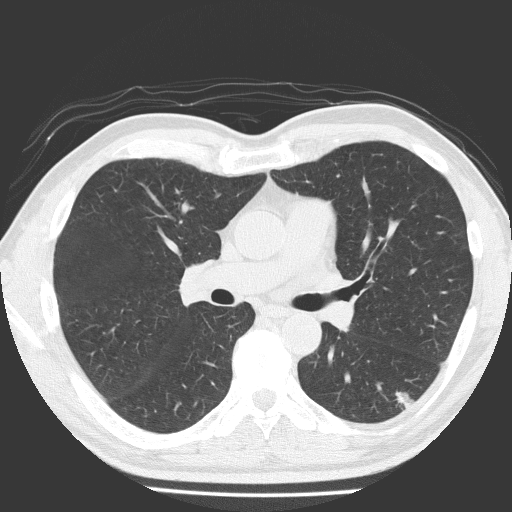
Low-dose screening chest CT, axial slice, baseline annual screen, lung window (W 1500 / L -600 HU), 2 mm slice thickness, lung (sharp) reconstruction kernel (FC51), slice 79 of 184 in the series. Male participant, aged 58 years at enrolment.
- Expert-annotated lung lesion, box from (x=365, y=374) to (x=427, y=423) px.
- The screening reader recorded 4 non-calcified nodules or masses ≥4 mm on this exam (left lower lobe, left lower lobe, right middle lobe, left upper lobe); which of them this box marks is not recorded.
- Later outcome: lung cancer diagnosed 99 days after this screen — adenosquamous carcinoma, left lower lobe, moderately differentiated (G2), stage IA (AJCC 6th edition), 28 mm at pathology.